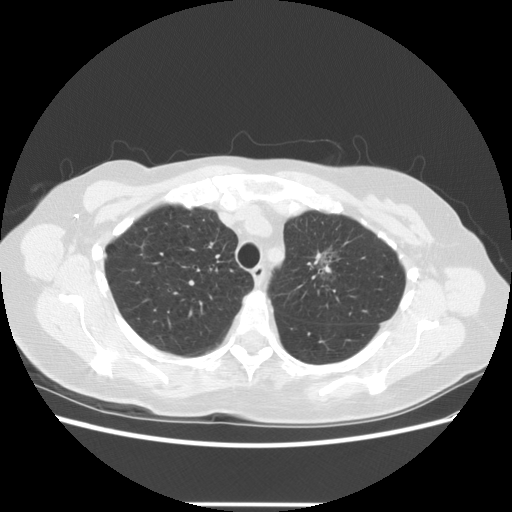
Axial slice from a low-dose chest CT screening exam, third annual screen, lung window (W 1500 / L -600 HU), slice 98 of 126 in the series. Female, age 65 years at enrolment. Former smoker at enrolment.
• Expert-annotated lung lesion, box from (x=291, y=224) to (x=370, y=294) px.
• Reader record for this screening exam (exam-level; its link to the box is not recorded): non-calcified nodule or mass ≥4 mm, left upper lobe, 17 × 14 mm, poorly defined margins, ground glass attenuation, pre-existing on the prior screen: yes; interval growth: yes.
• Official screen result: positive, other.
• Lung cancer was diagnosed 96 days after this screen: adenocarcinoma, NOS, left upper lobe, moderately differentiated (G2), stage IA (AJCC 6th edition), 30 mm at pathology.